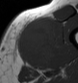
MRI of an extremity soft-tissue mass, one axial slice; slice 22 of 43 in the series (ordered by position); MR volume resampled by the dataset authors to the PET/CT grid (not the native acquisition matrix); 3.27 mm slice thickness; 78 × 83 image matrix, field of view 76 × 81 mm. Male patient. From the clinical record (not read from this slice): histological type: pleiomorphic leiomyosarcoma; grade: high; site of the primary tumour: left thigh.
Annotated regions visible in this slice (expert contour drawn on MRI and transferred to this co-registered scan by the dataset authors):
- gross tumour volume including surrounding oedema: bounding box (x1, y1, x2, y2) in pixels: (15, 17, 60, 64)
- gross tumour volume (mass): (15, 19, 57, 64)